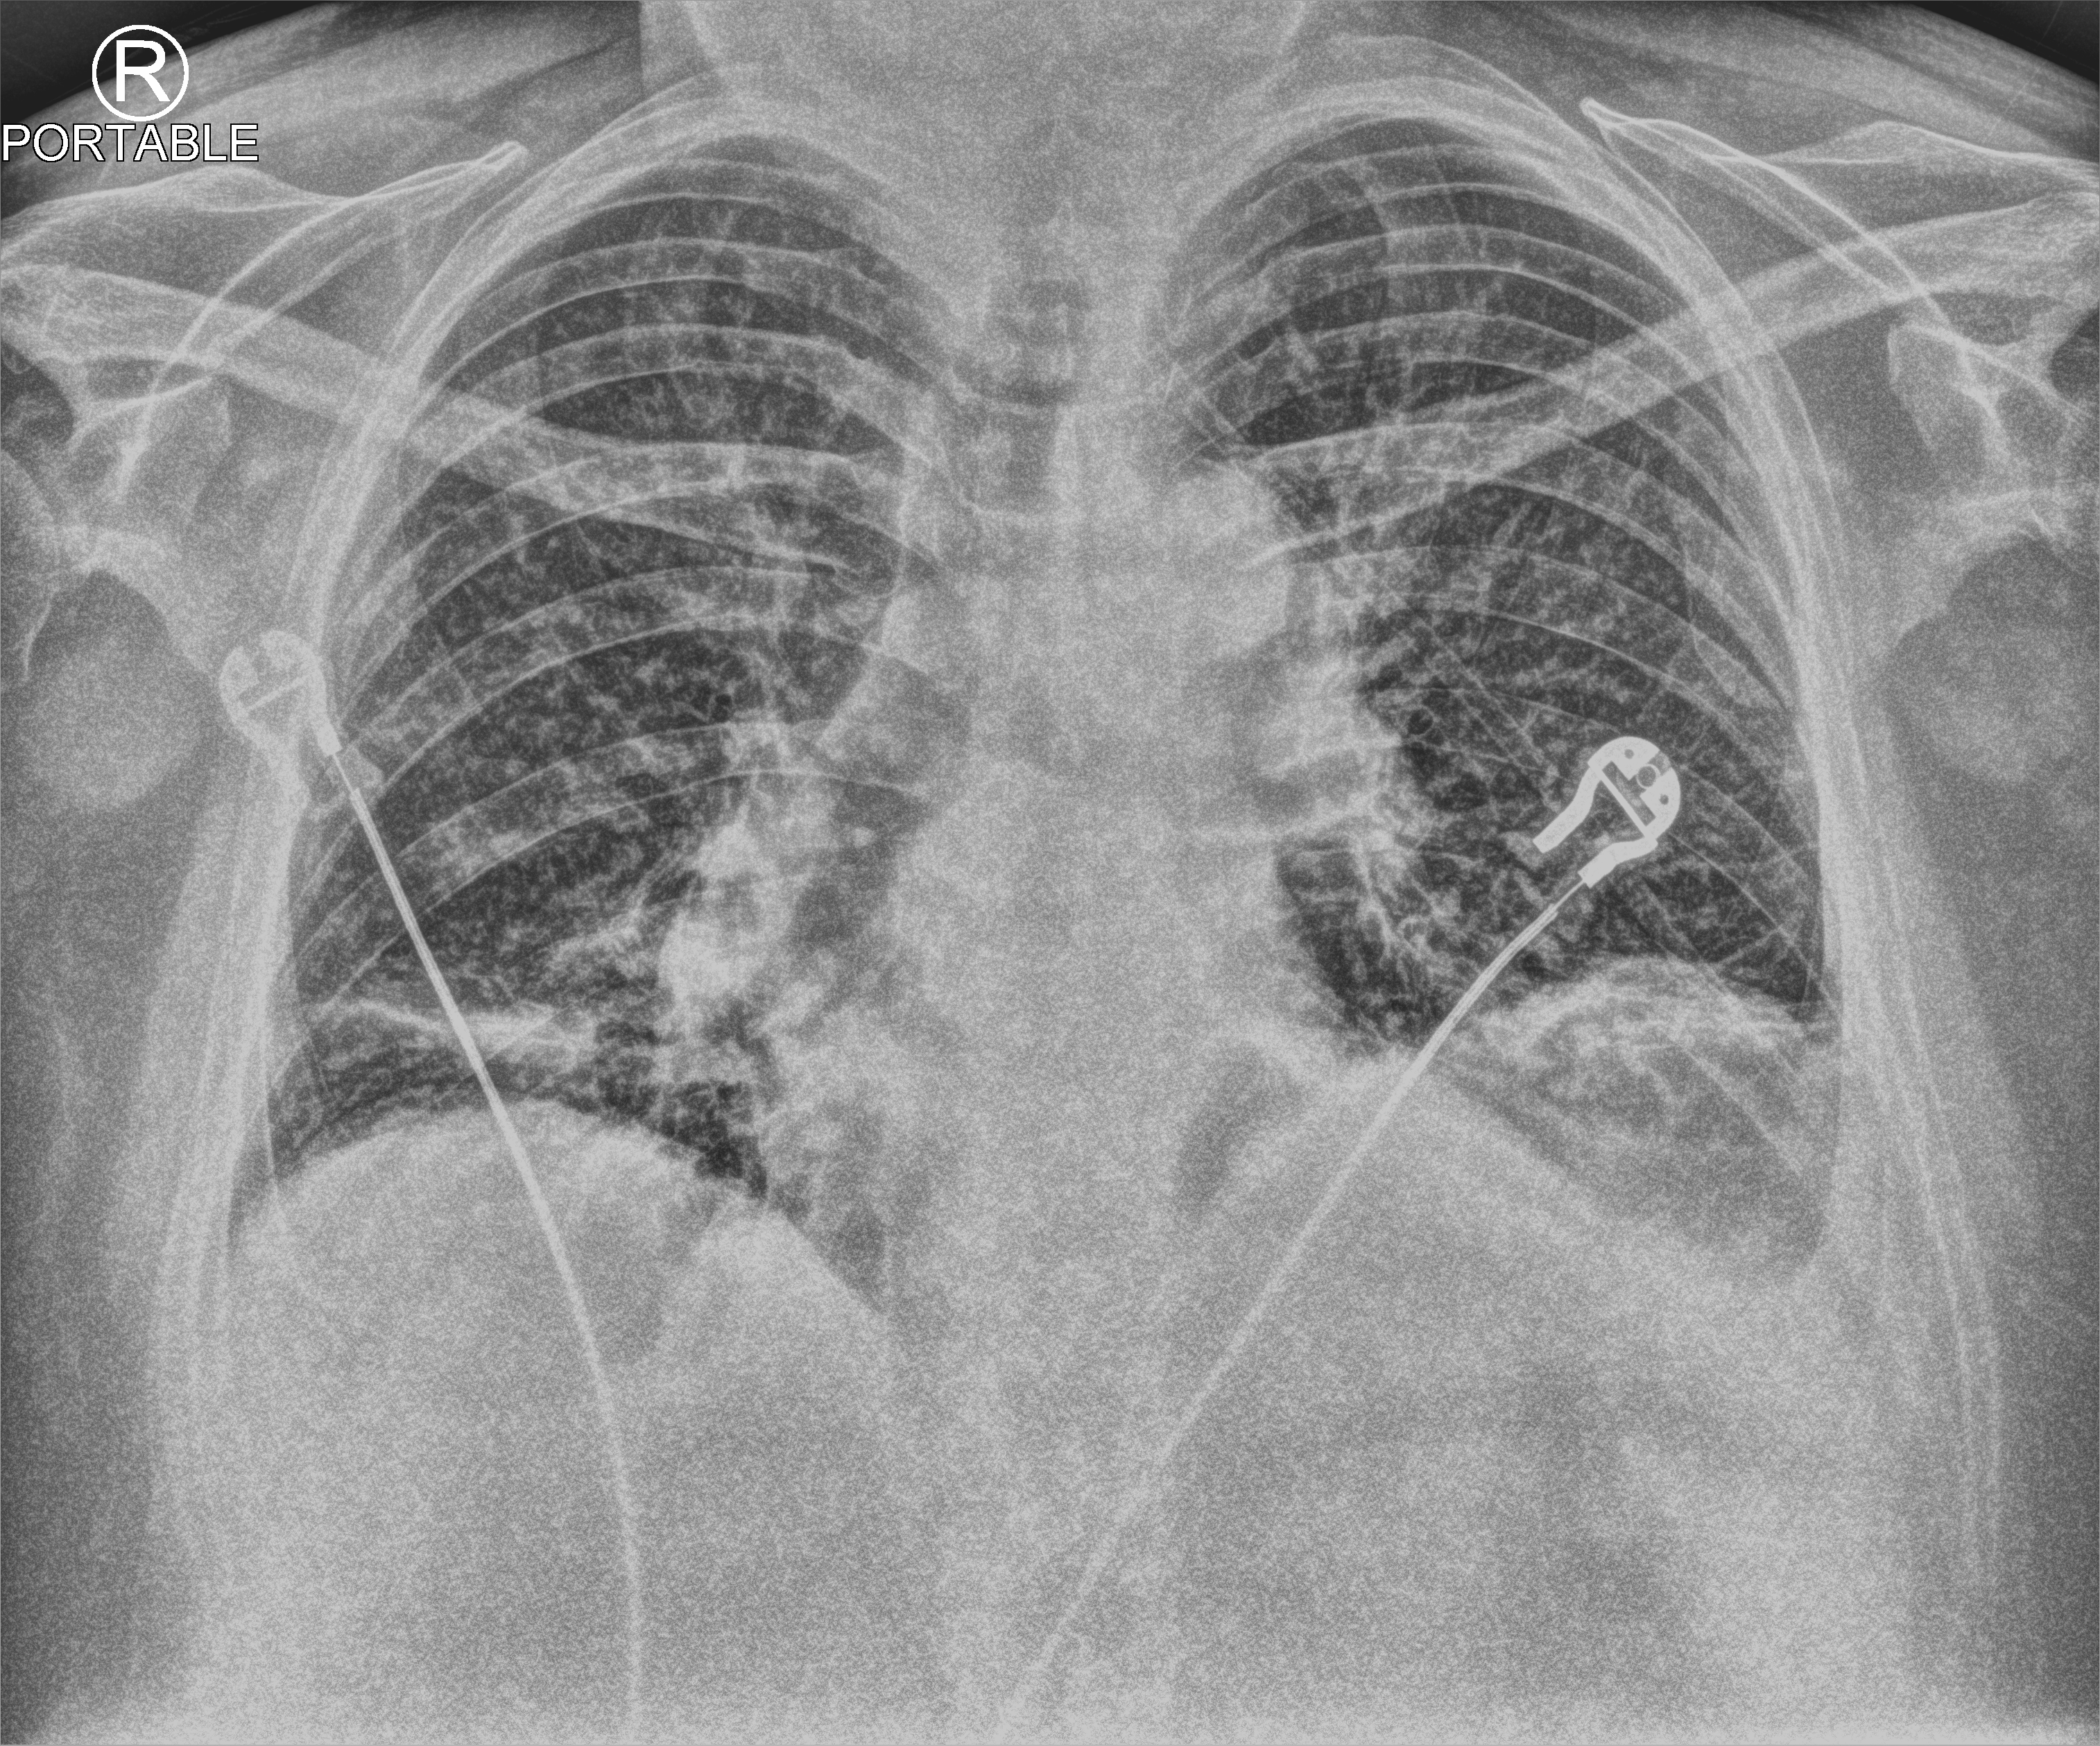
Chest X-ray (portable); anteroposterior (AP) projection. Patient hospitalised with COVID-19; male, aged 60–74 years.
Hospital-stay facts (about this admission, not read from this image; timing relative to this image not recorded): length of hospital stay: 22 days.